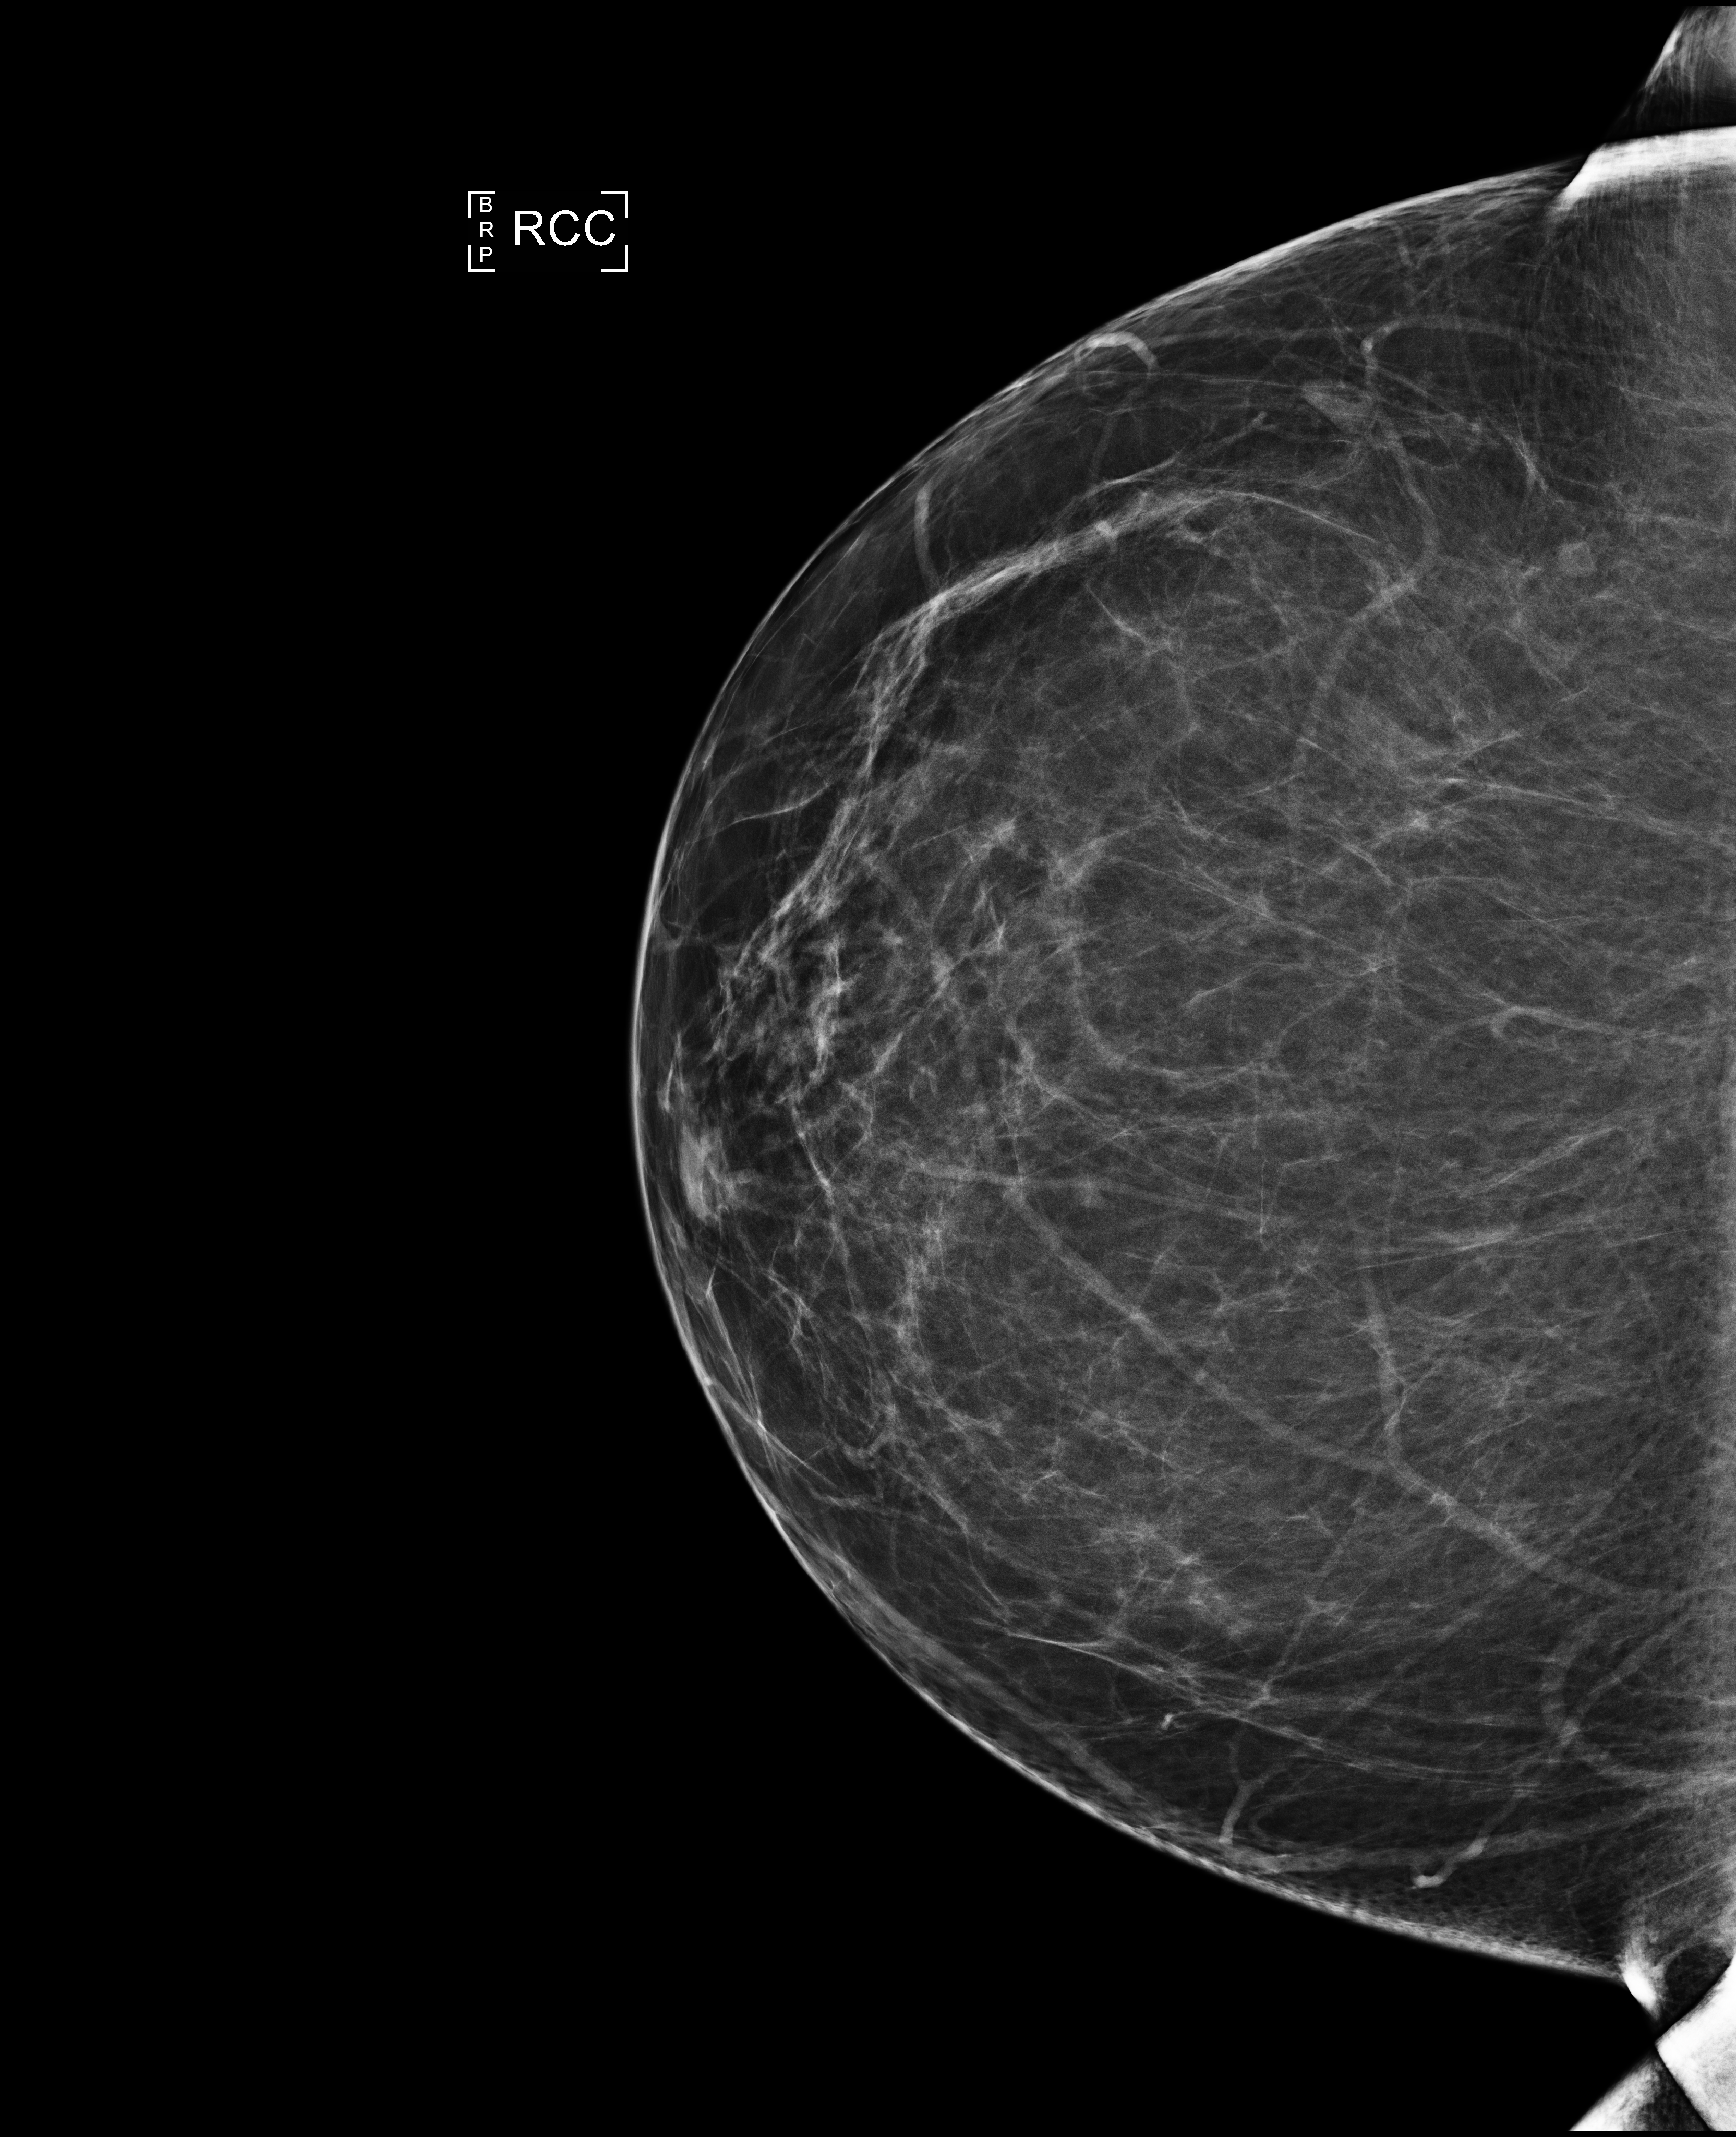
Screening examination. Patient: female, 51 years.
Image type: full-field digital mammogram. Breast: right. Projection: cranio-caudal projection.